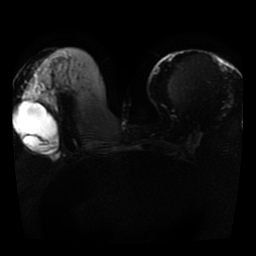
Breast MRI, one axial slice; position 14 of 41 along the scan axis; diffusion-weighted series; image 2 of 4 stored at this slice position (different b-values; order by instance number); 1.5 T; 5 mm slice thickness; 256 × 256 image matrix. Female patient.
Structures marked on this image (outlined manually by an expert reader):
- tumour on diffusion-weighted imaging: bounding box [x1, y1, x2, y2] px = [25, 90, 54, 112]